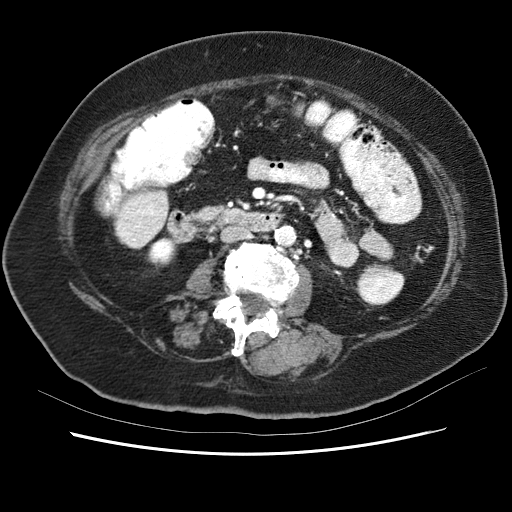
Contrast-enhanced abdominal CT (liver protocol), one axial slice. Slice 8 of 62 in the series (ordered by position). Reconstruction kernel STANDARD. Soft-tissue window (W 400 / L 40 HU). 2.5 mm slice thickness. 512 × 512 image matrix, field of view 340 × 340 mm. From the clinical record (not read from this slice): diagnosis: hepatocellular carcinoma (patient treated with transarterial chemoembolisation; whether this scan precedes or follows treatment is not stated here); TNM stage (as recorded): Stage-I; Child-Pugh class: B.
Outlined on this slice (semi-automatically segmented with operator editing):
- liver parenchyma outside the tumour (the mass and vessels are separate outlines, so this box may not span the whole liver): bounding box <128,192,154,205> (left, top, right, bottom; pixels)